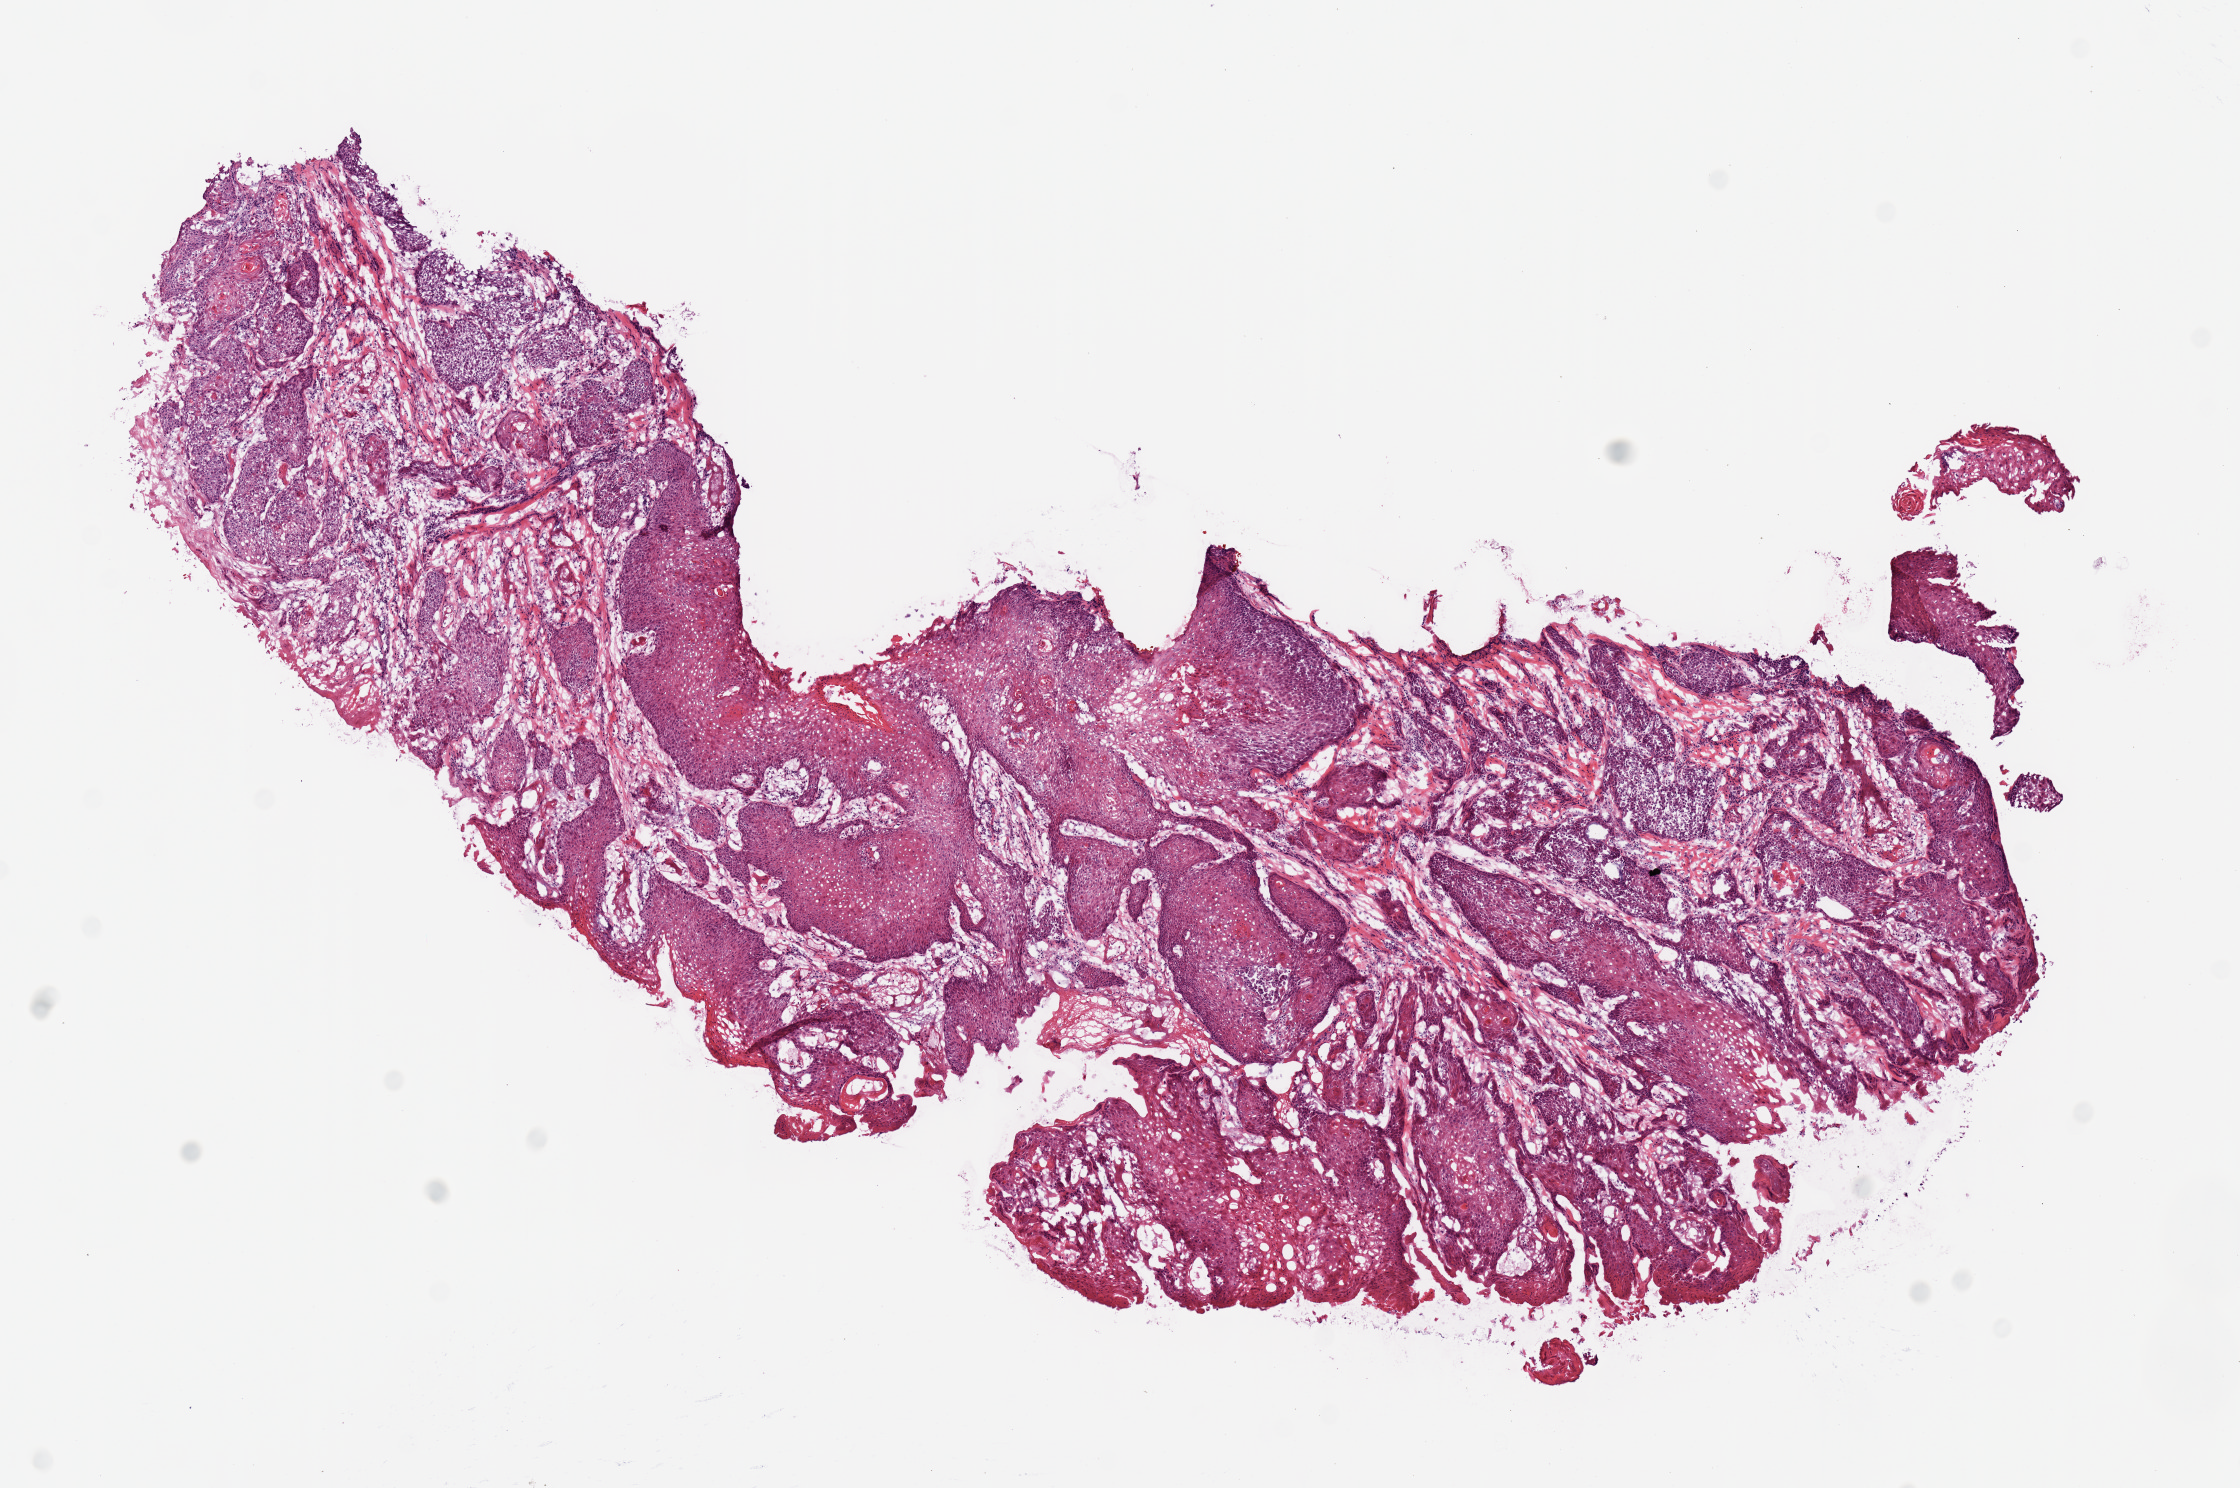
Digitized H&E-stained tissue section (whole slide), whole scanned area (about 8.9 x 5.9 mm, acquisition: 20x scan) shown as a low-resolution overview; frozen section; primary tumour sample from the head and neck. Patient: female, age at initial diagnosis 85 years.
Diagnosis: Squamous cell carcinoma, NOS.